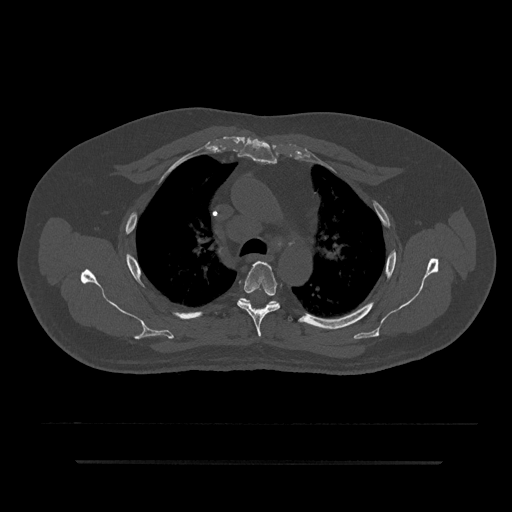
CT including the spine, one axial slice. Position 610 of 797 along the scan axis. Reconstruction kernel Br40s/3. Bone window (W 1800 / L 400 HU). 512 × 512 image matrix, field of view 464 × 464 mm. Male patient, age 59 years. From the clinical record (not read from this slice): primary cancer: bile ducts; vertebrae with lytic lesions (as recorded): T10.
Outlined on this slice (semi-automatically segmented with operator editing):
- T4 vertebra: bounding box <237,261,280,337> (left, top, right, bottom; pixels)
- T5 vertebra: <237,298,300,322>